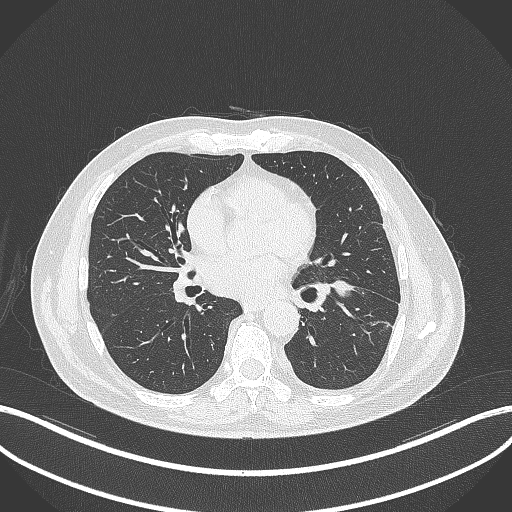
Chest CT, one axial slice; position 173 of 230 along the scan axis; lung window (W 1500 / L -600 HU); 512 × 512 image matrix. Patient: male, 68 years. Case-level facts recorded for this patient, not image findings: clinical TNM (as recorded): T2b N0 M0.
Outlined on this slice (rectangle marked by the reading radiologist):
- lung tumour (recorded histology: squamous cell carcinoma): box from (x=329, y=276) to (x=359, y=301) px